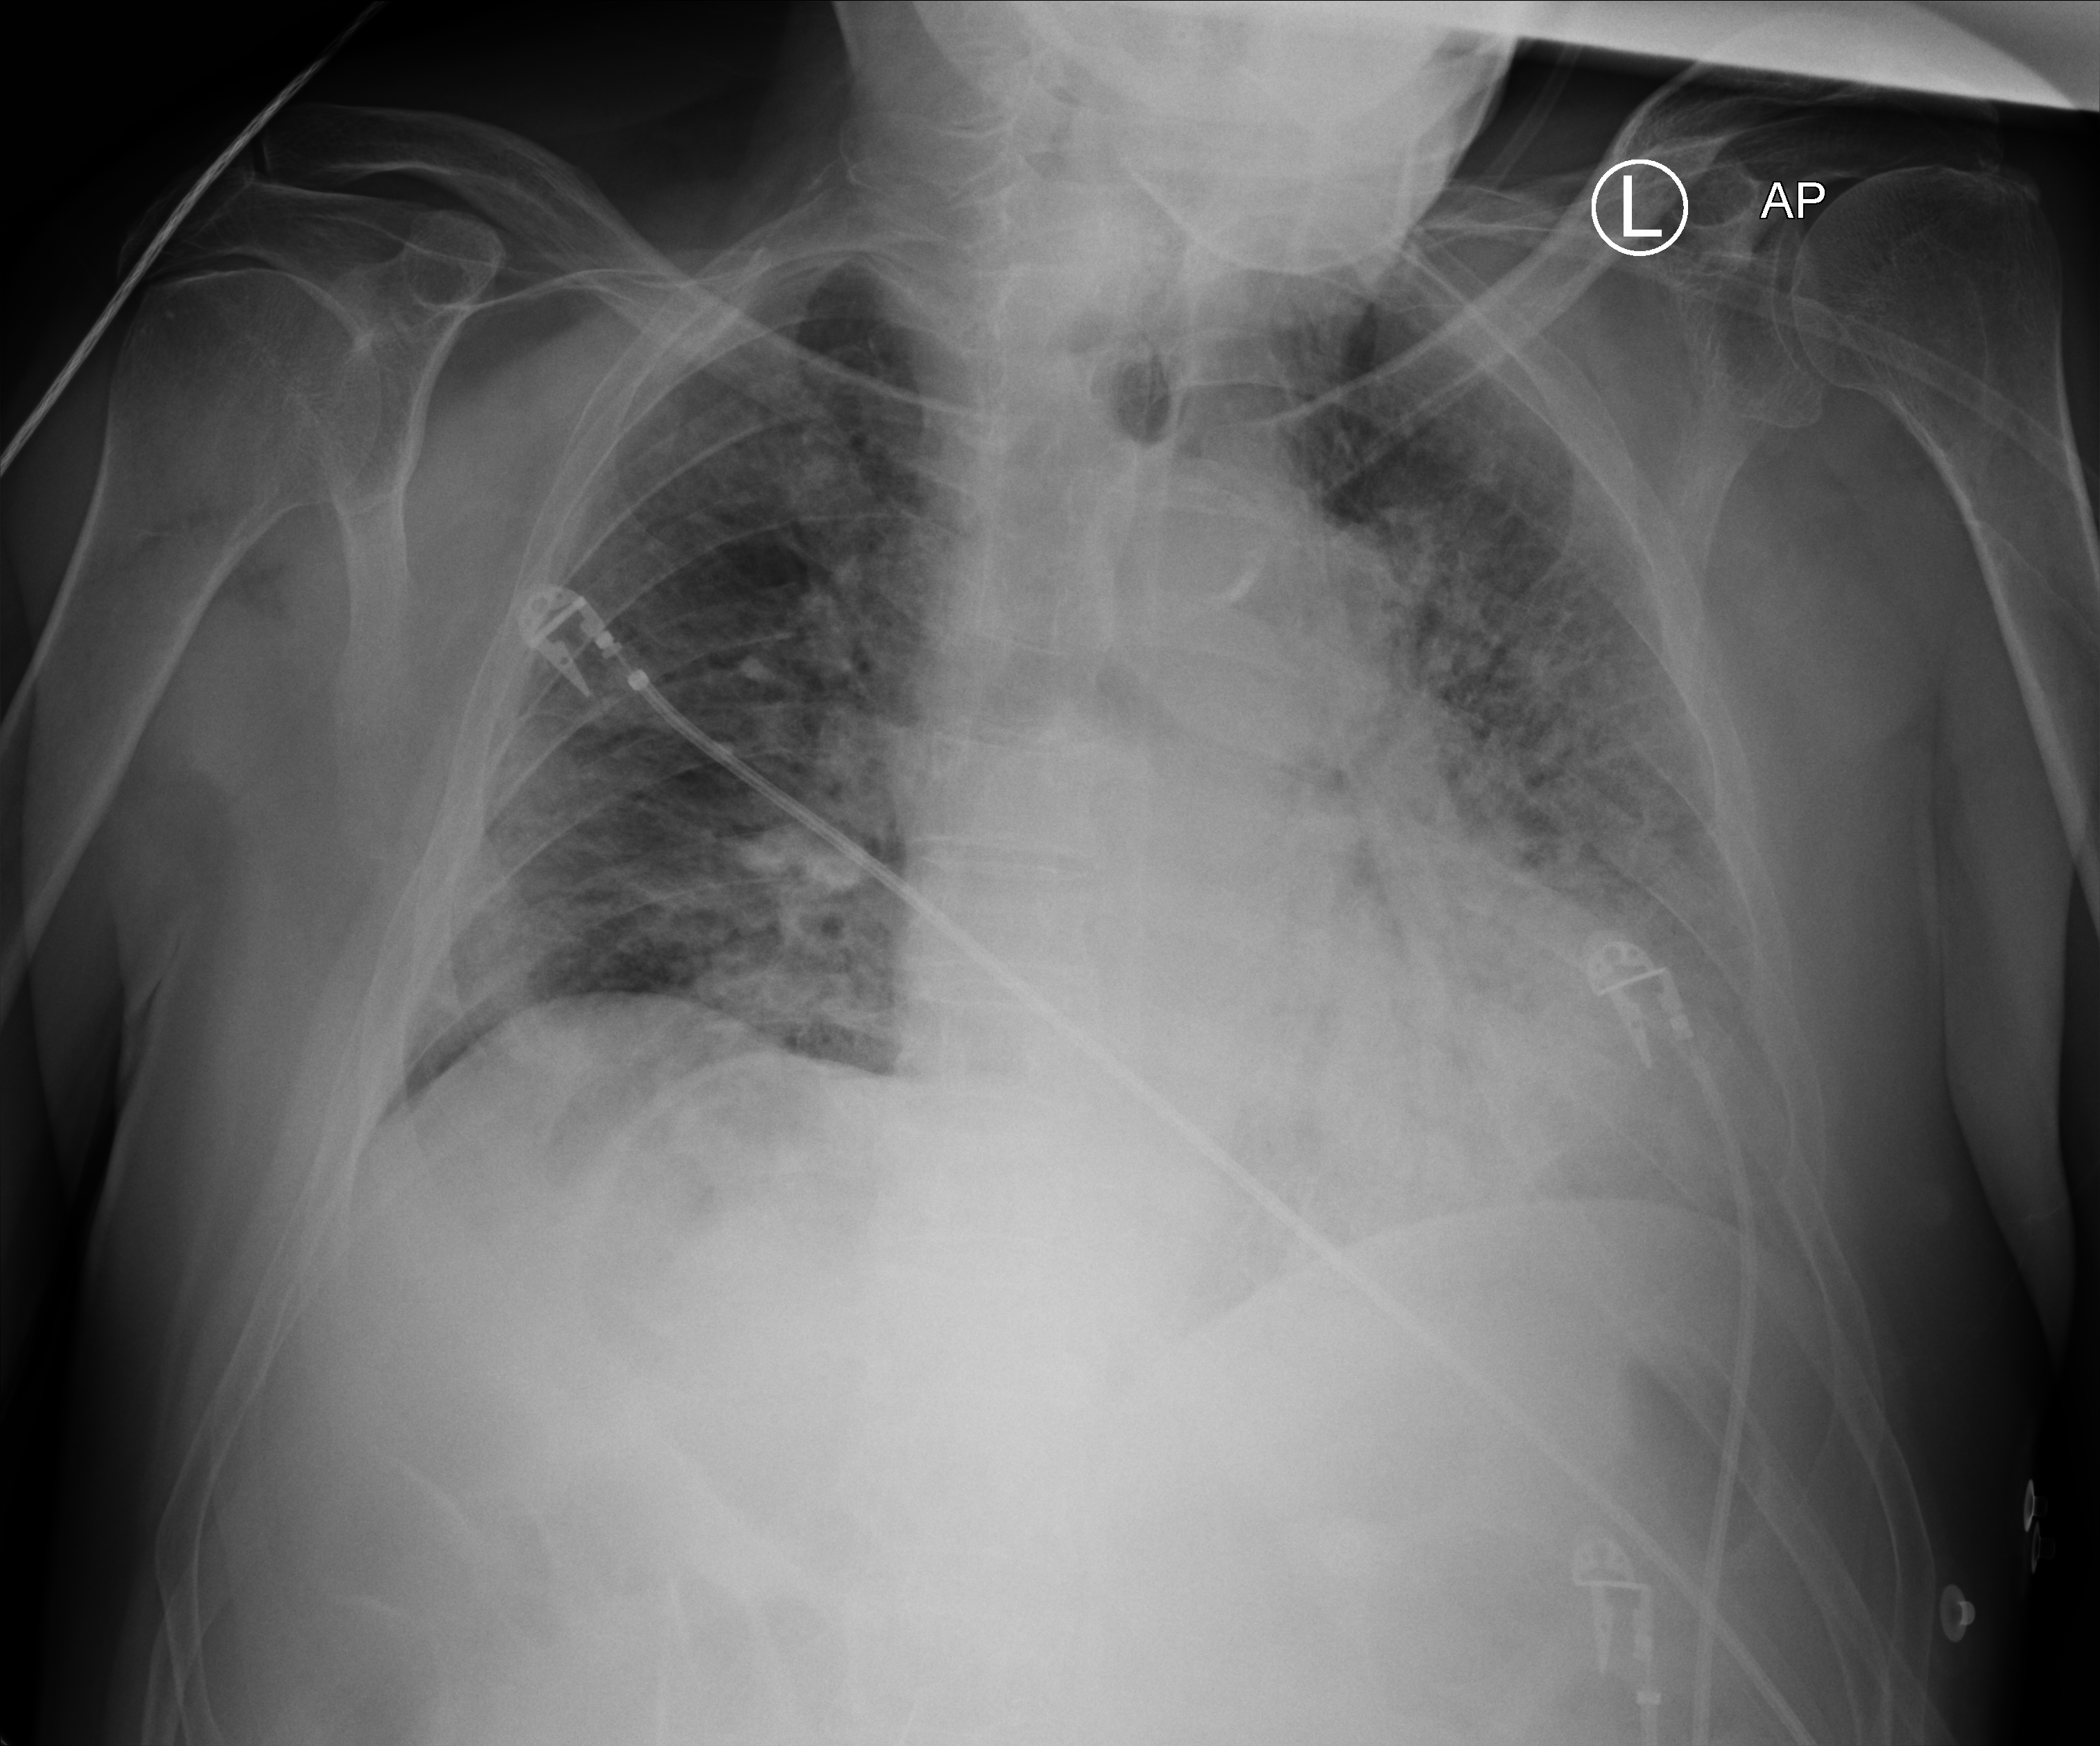
Portable chest radiograph; anteroposterior (AP) projection. Male patient hospitalised with COVID-19, age 60–74 years.
From the hospital-stay record, not from the radiograph (when in the stay this image was taken is not recorded):
- mechanically ventilated during this hospital stay: yes
- chronic kidney disease (admission record): no